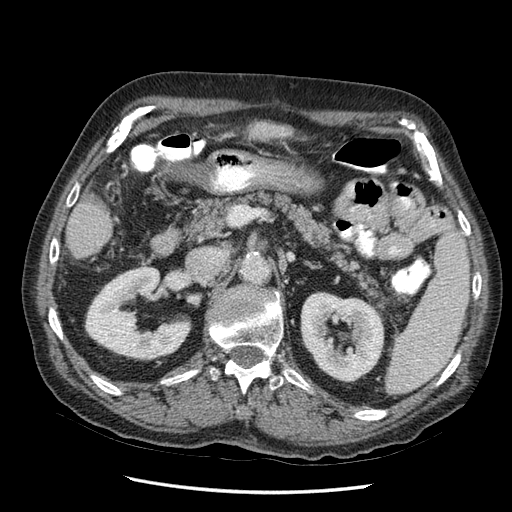
Contrast-enhanced abdominal CT (liver protocol), one axial slice. Slice 12 of 67 in the series (ordered by position). Reconstruction kernel STANDARD. 120 kVp. Soft-tissue window (W 400 / L 40 HU). 2.5 mm slice thickness. 512 × 512 image matrix, field of view 360 × 360 mm. Case-level facts recorded for this patient, not image findings: diagnosis: hepatocellular carcinoma (patient treated with transarterial chemoembolisation; whether this scan precedes or follows treatment is not stated here); TNM stage (as recorded): Stage-I; Child-Pugh class: A.
Annotated regions visible in this slice (semi-automatically segmented with operator editing):
- liver parenchyma outside the tumour (the mass and vessels are separate outlines, so this box may not span the whole liver): box from (x=230, y=120) to (x=302, y=148) px